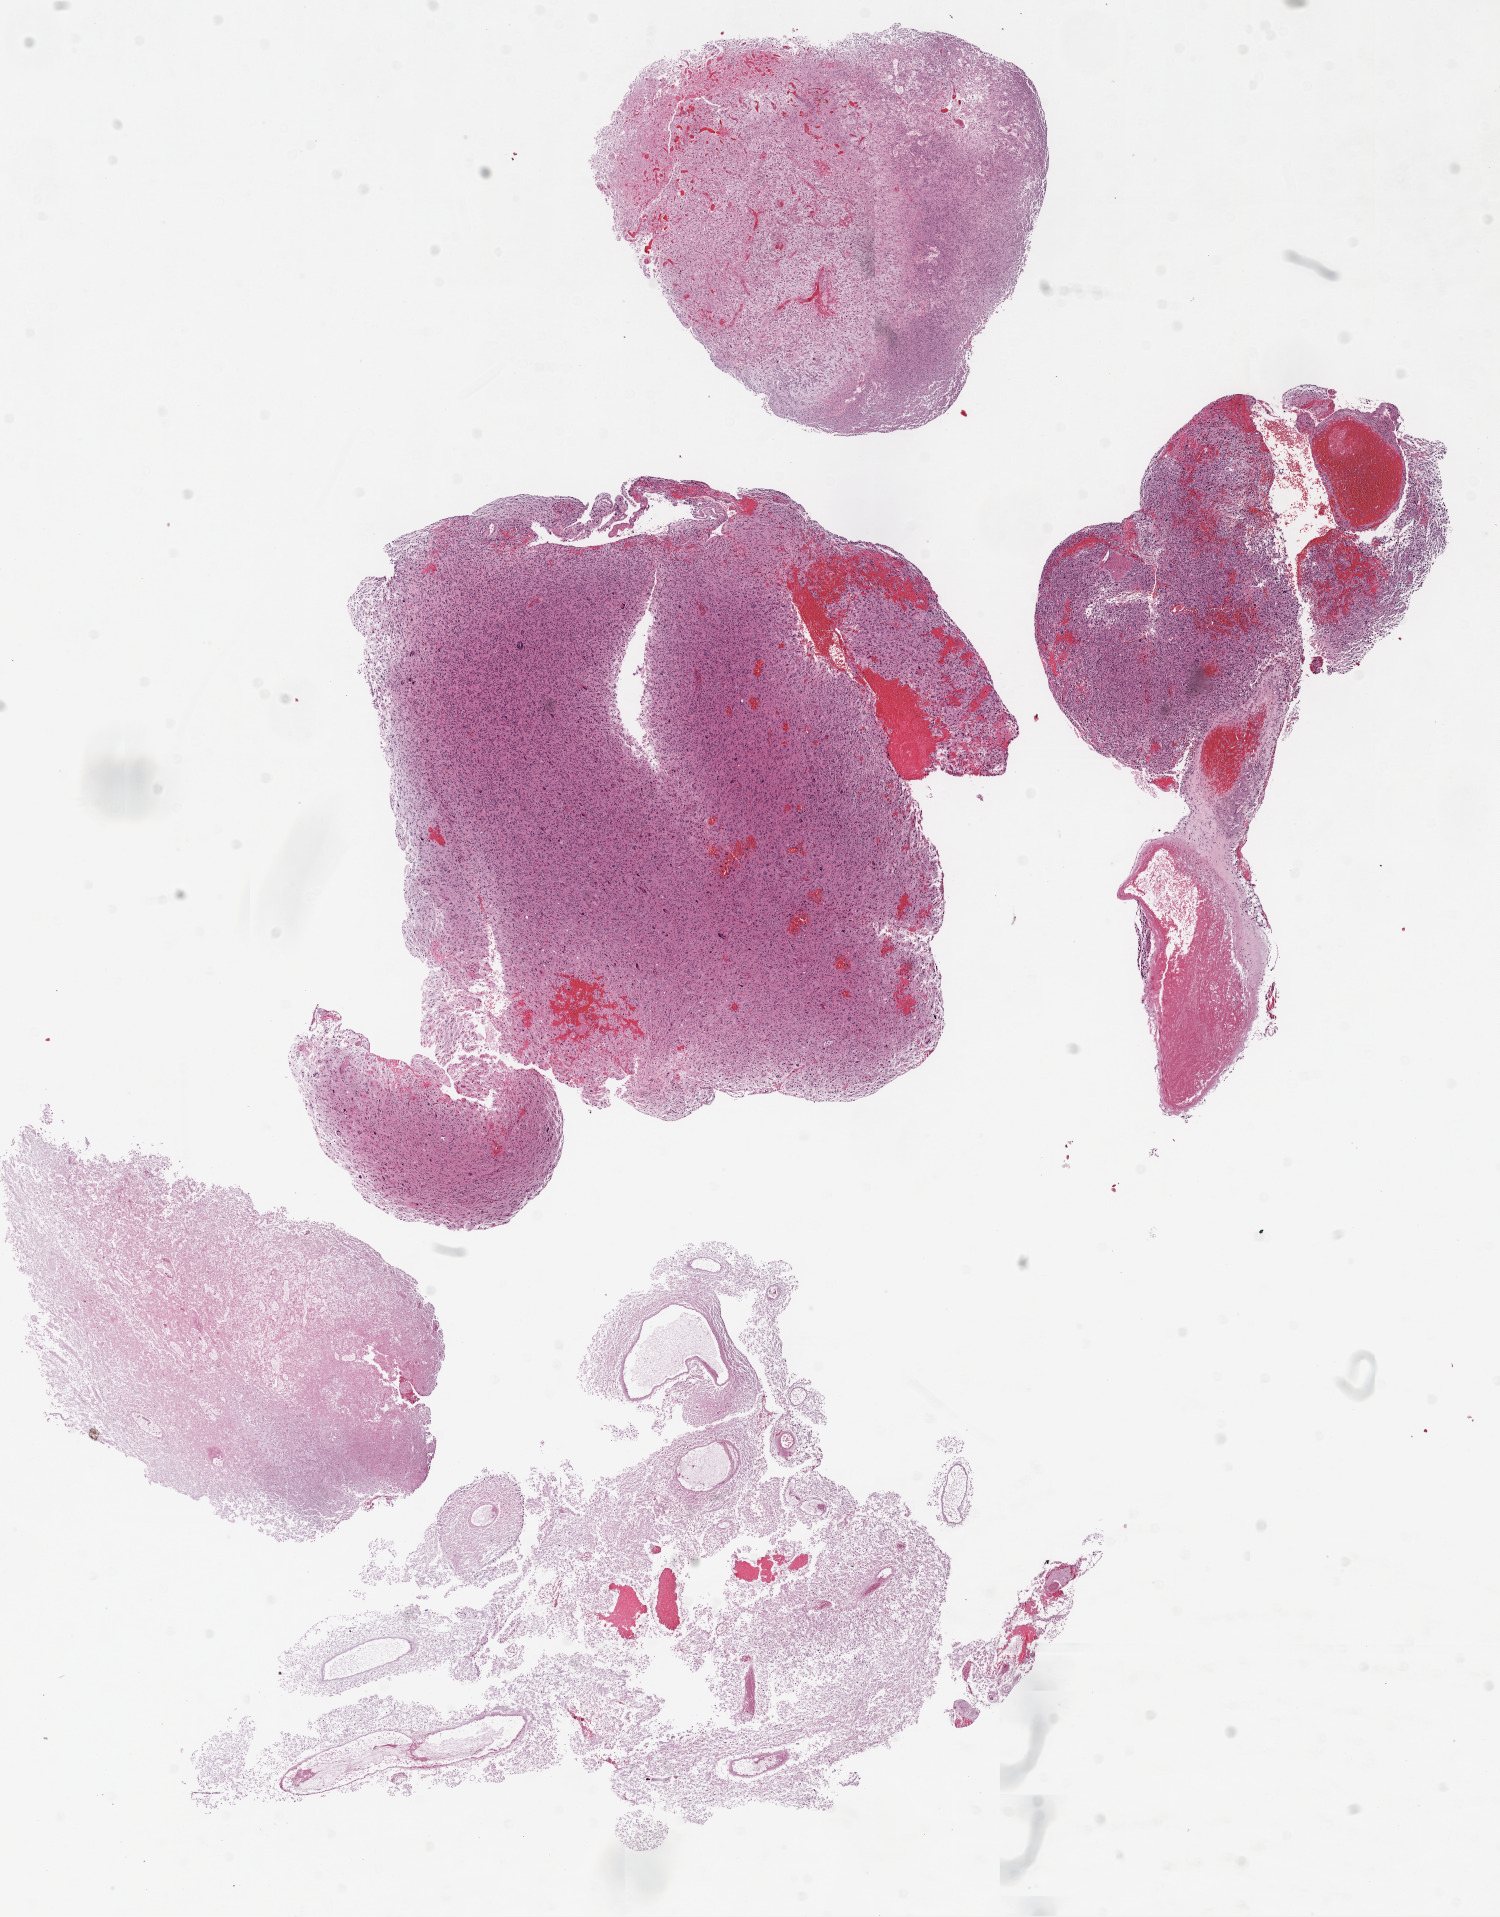
Whole-slide histology image, Hematoxylin and eosin (H&E) stained, low-resolution overview of the scanned area, about 12.0 x 15.4 mm (from a 20x scan). FFPE section. Brain, primary tumour sample. Male patient; age at initial diagnosis 59 years.
Diagnosis: Glioblastoma.